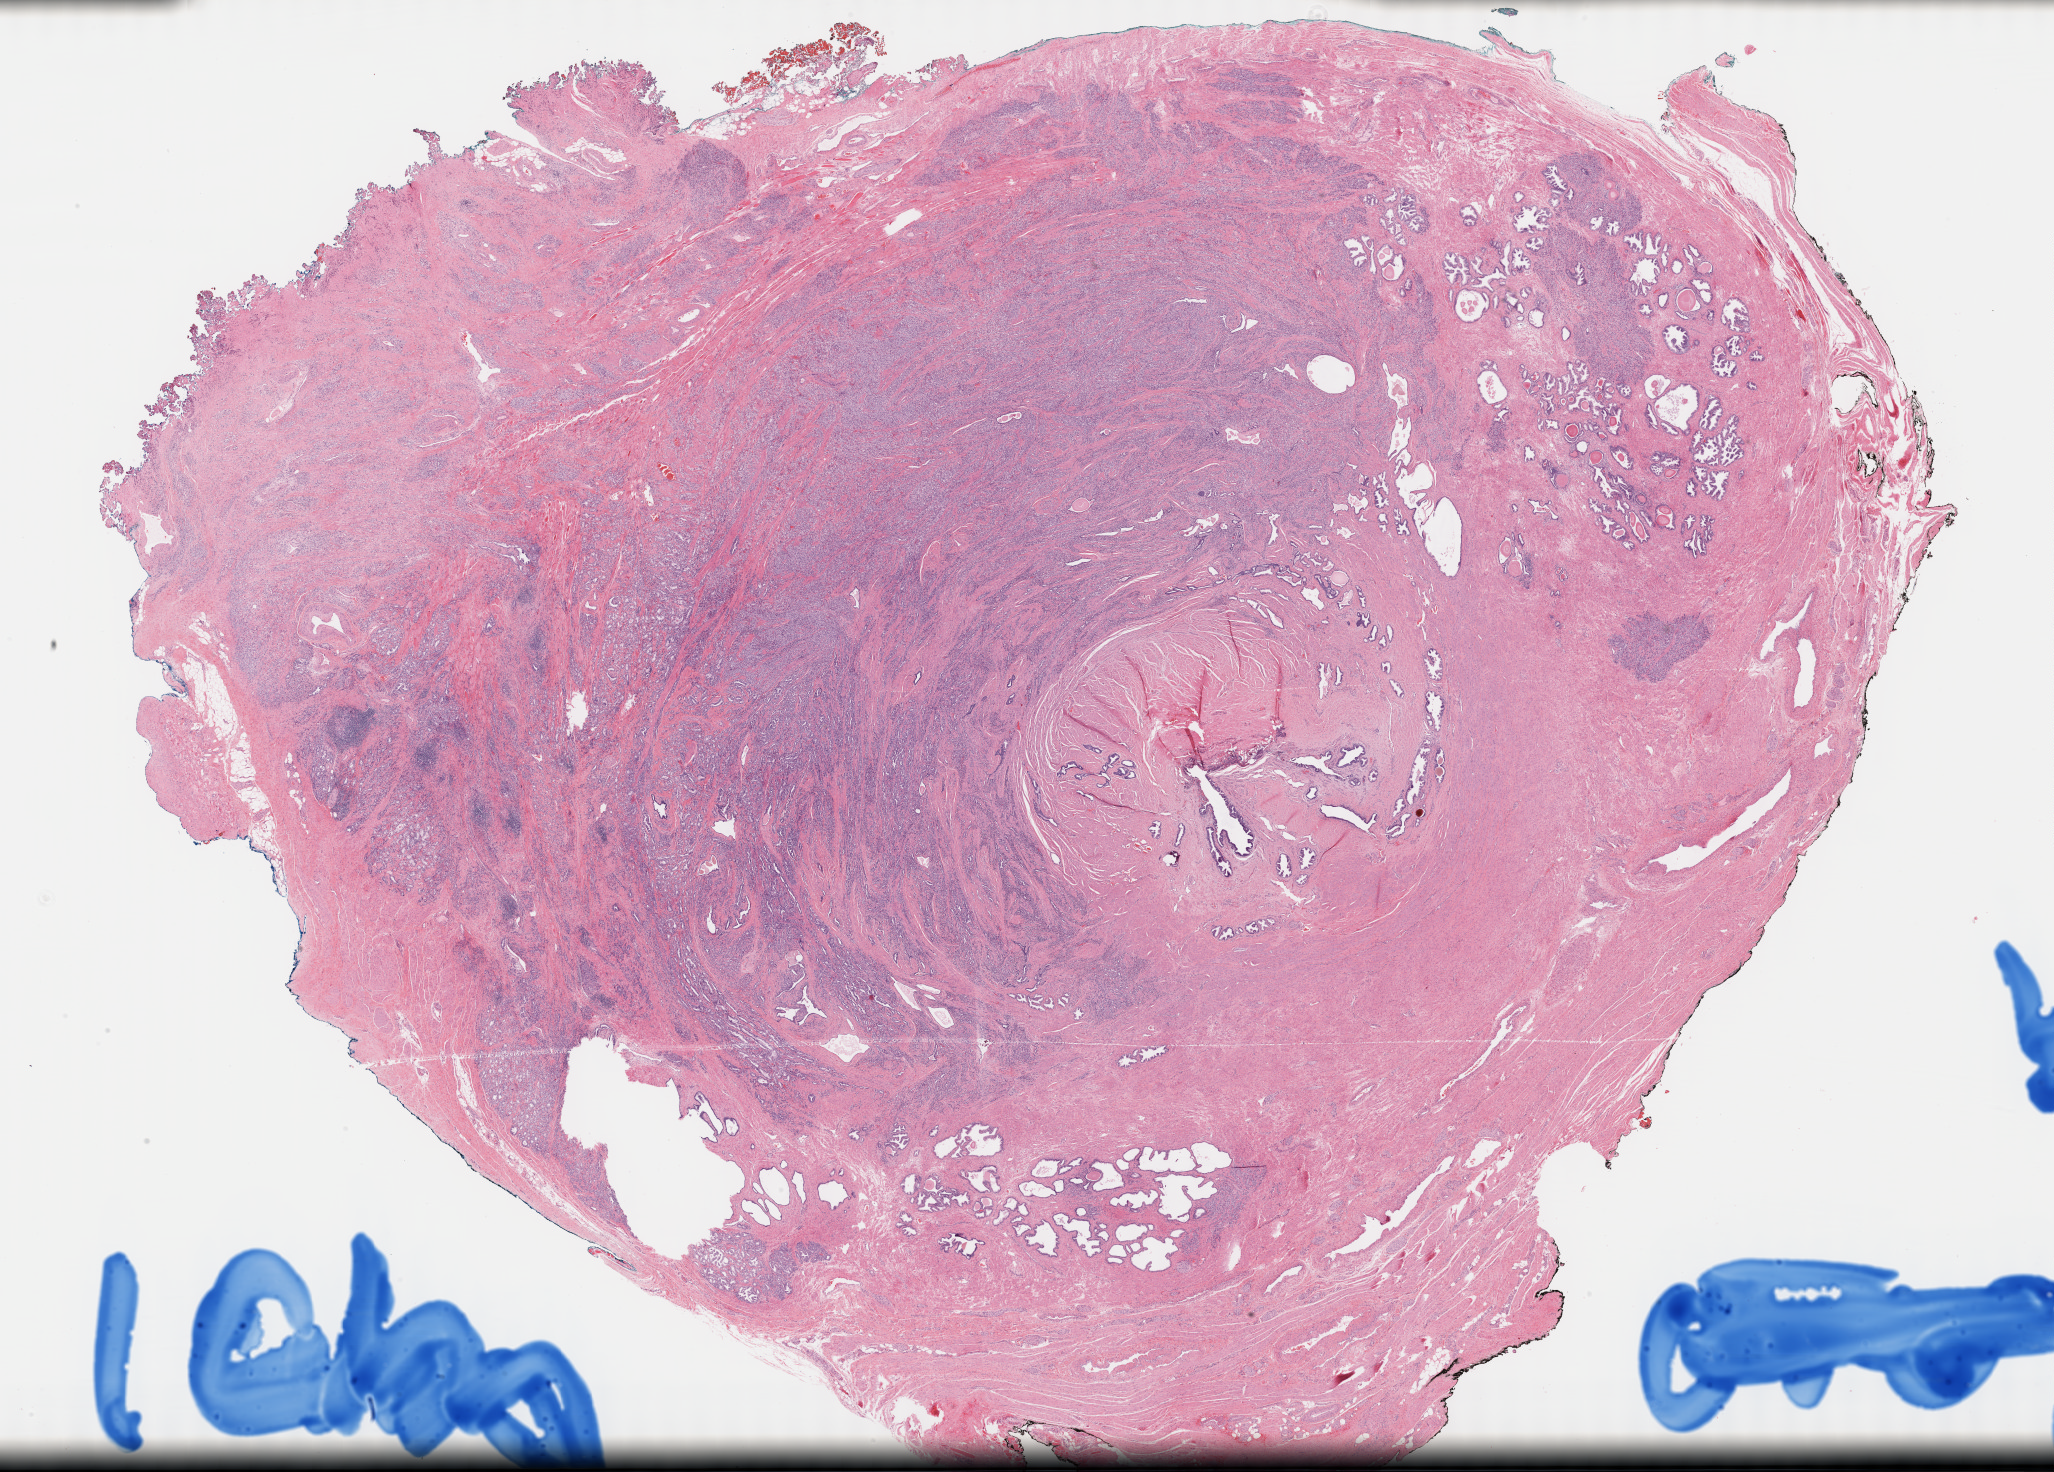
H&E whole-slide image, a low-resolution overview of the entire scanned area, about 33.2 x 23.8 mm (slide scanned at 40x). Formalin-fixed paraffin-embedded (FFPE) diagnostic section. Primary tumour sample from the prostate. Male, age 59 years at initial diagnosis. Gleason score: 9 (5+4).
Histologic diagnosis: Adenocarcinoma, NOS. Lymph nodes positive (case pathology): 0 of 18 examined. Laterality: bilateral.